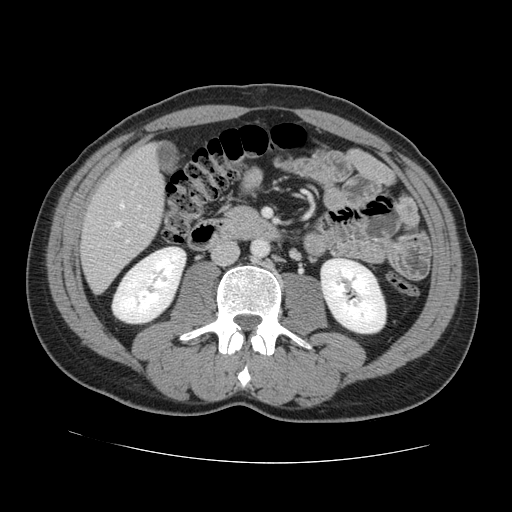
Contrast-enhanced abdominal CT, one axial slice. Position 38 of 131 along the scan axis. 120 kVp. Intravenous contrast given. Soft-tissue window (W 400 / L 40 HU). 2.5 mm slice thickness. 512 × 512 image matrix, field of view 380 × 380 mm. Male patient, age 40 years. Case-level facts recorded for this patient, not image findings: diagnosis: colorectal cancer liver metastases, imaged before liver resection; multiple liver metastases: yes; largest metastasis: 2.9 cm; disease in both lobes: yes.
Structures marked on this image (expert manual segmentation):
- hepatic veins: bounding box (x1, y1, x2, y2) in pixels: (115, 203, 140, 226)
- liver: (82, 146, 163, 291)
- planned liver remnant (the part of the liver to remain after resection): (136, 146, 156, 162)
- portal vein (with intrahepatic branches): (126, 240, 129, 243)